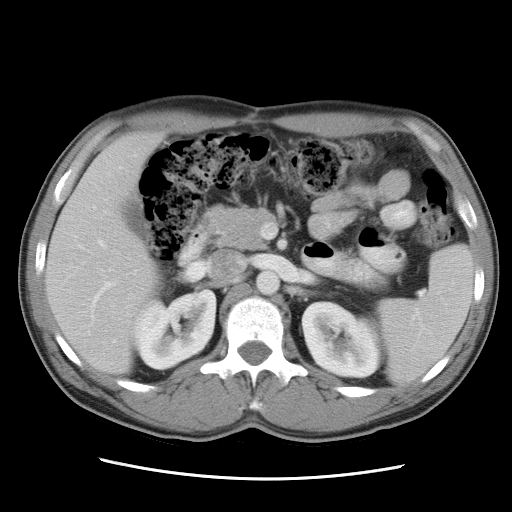
Contrast-enhanced abdominal CT, one axial slice; position 15 of 34 along the scan axis; reconstruction kernel STANDARD; 120 kVp; soft-tissue window (W 400 / L 40 HU); 7.5 mm slice thickness; 512 × 512 image matrix. Male patient, age 40 years. Case-level facts recorded for this patient, not image findings: diagnosis: colorectal cancer liver metastases, imaged before liver resection; multiple liver metastases: yes.
Structures marked on this image (manually delineated by an expert):
- liver: bounding box <47,133,165,375> (left, top, right, bottom; pixels)
- planned liver remnant (the part of the liver to remain after resection): <47,133,164,374>
- portal vein (with intrahepatic branches): <94,241,111,304>